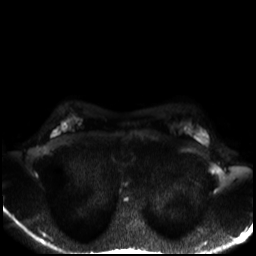
Breast MRI, one axial slice. Slice 20 of 30 in the series (ordered by position). Diffusion-weighted series; image 2 of 4 stored at this slice position (different b-values; order by instance number). 3 T. 4 mm slice thickness. 256 × 256 image matrix, field of view 320 × 320 mm. Female patient.
Annotated regions visible in this slice (expert manual segmentation):
- tumour on diffusion-weighted imaging: bounding box <199,132,207,143> (left, top, right, bottom; pixels)